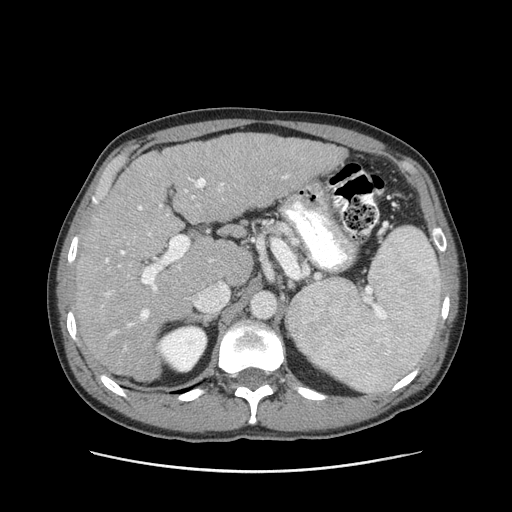
Contrast-enhanced abdominal CT (liver protocol), one axial slice; slice 59 of 93 in the series (ordered by position); soft-tissue window (W 400 / L 40 HU); 2.5 mm slice thickness; 512 × 512 image matrix, field of view 380 × 380 mm. Case-level facts recorded for this patient, not image findings: diagnosis: hepatocellular carcinoma (patient treated with transarterial chemoembolisation; whether this scan precedes or follows treatment is not stated here); TNM stage (as recorded): Stage-II; Child-Pugh class: A; tumour differentiation: moderately differentiated; tumour nodularity: multinodular.
Annotated regions visible in this slice (semi-automatically segmented with operator editing):
- liver parenchyma outside the tumour (the mass and vessels are separate outlines, so this box may not span the whole liver): box from (x=74, y=134) to (x=345, y=380) px
- liver vessels: (x=105, y=175)–(x=288, y=336)